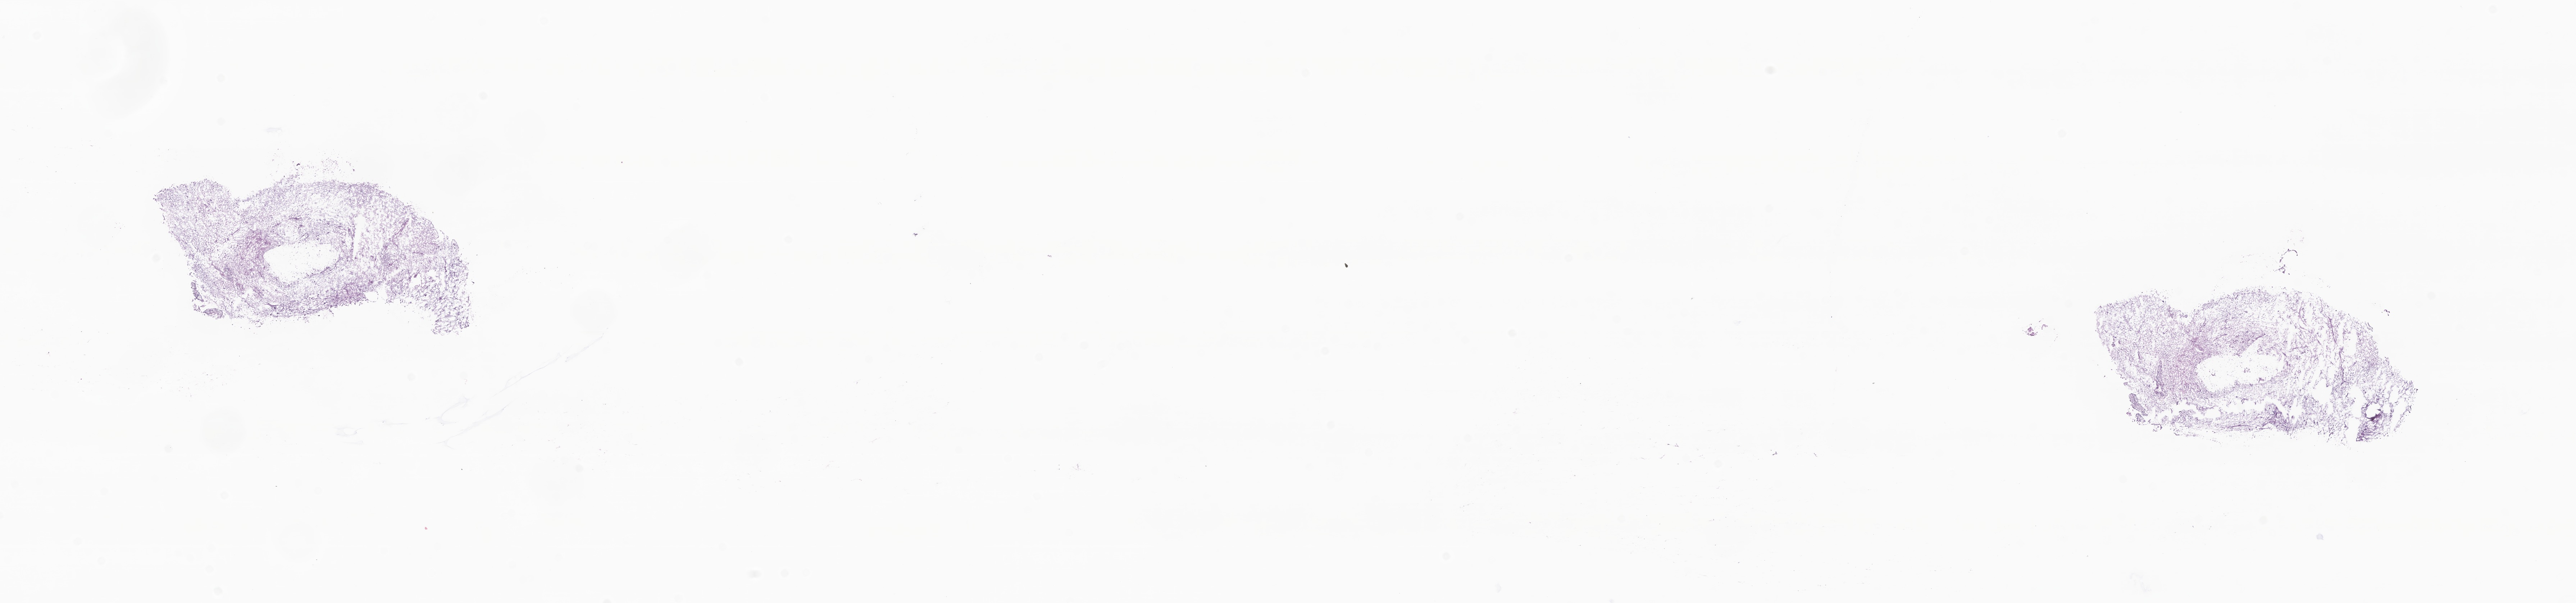
Whole-slide image, hematoxylin and eosin (H&E) stain of tumor tissue from the brain — low-resolution overview of the scanned area, about 30.2 x 7.1 mm. Cryosection (OCT / tissue freezing medium). Patient male; age 217 months.
Recorded diagnosis: Ganglioglioma, NOS.